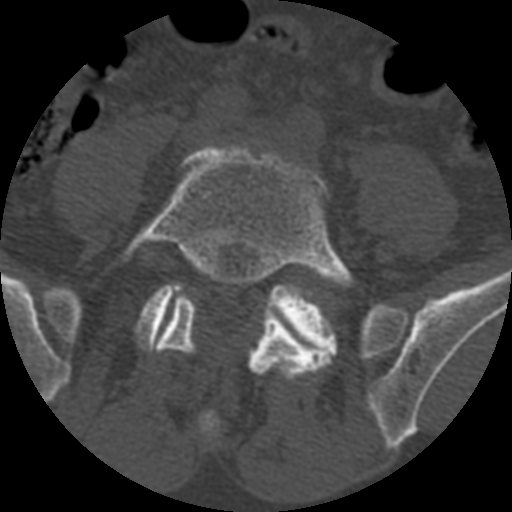
CT including the spine, one axial slice; position 253 of 399 along the scan axis; reconstruction kernel STANDARD; 120 kVp; bone window (W 1800 / L 400 HU); 1.25 mm slice thickness; 512 × 512 image matrix, field of view 160 × 160 mm. Patient age 71 years. Case-level facts recorded for this patient, not image findings: primary cancer: prostate.
Outlined on this slice (semi-automatic segmentation, software-assisted and operator-edited):
- L5 vertebra: bounding box <121,145,357,381> (left, top, right, bottom; pixels)